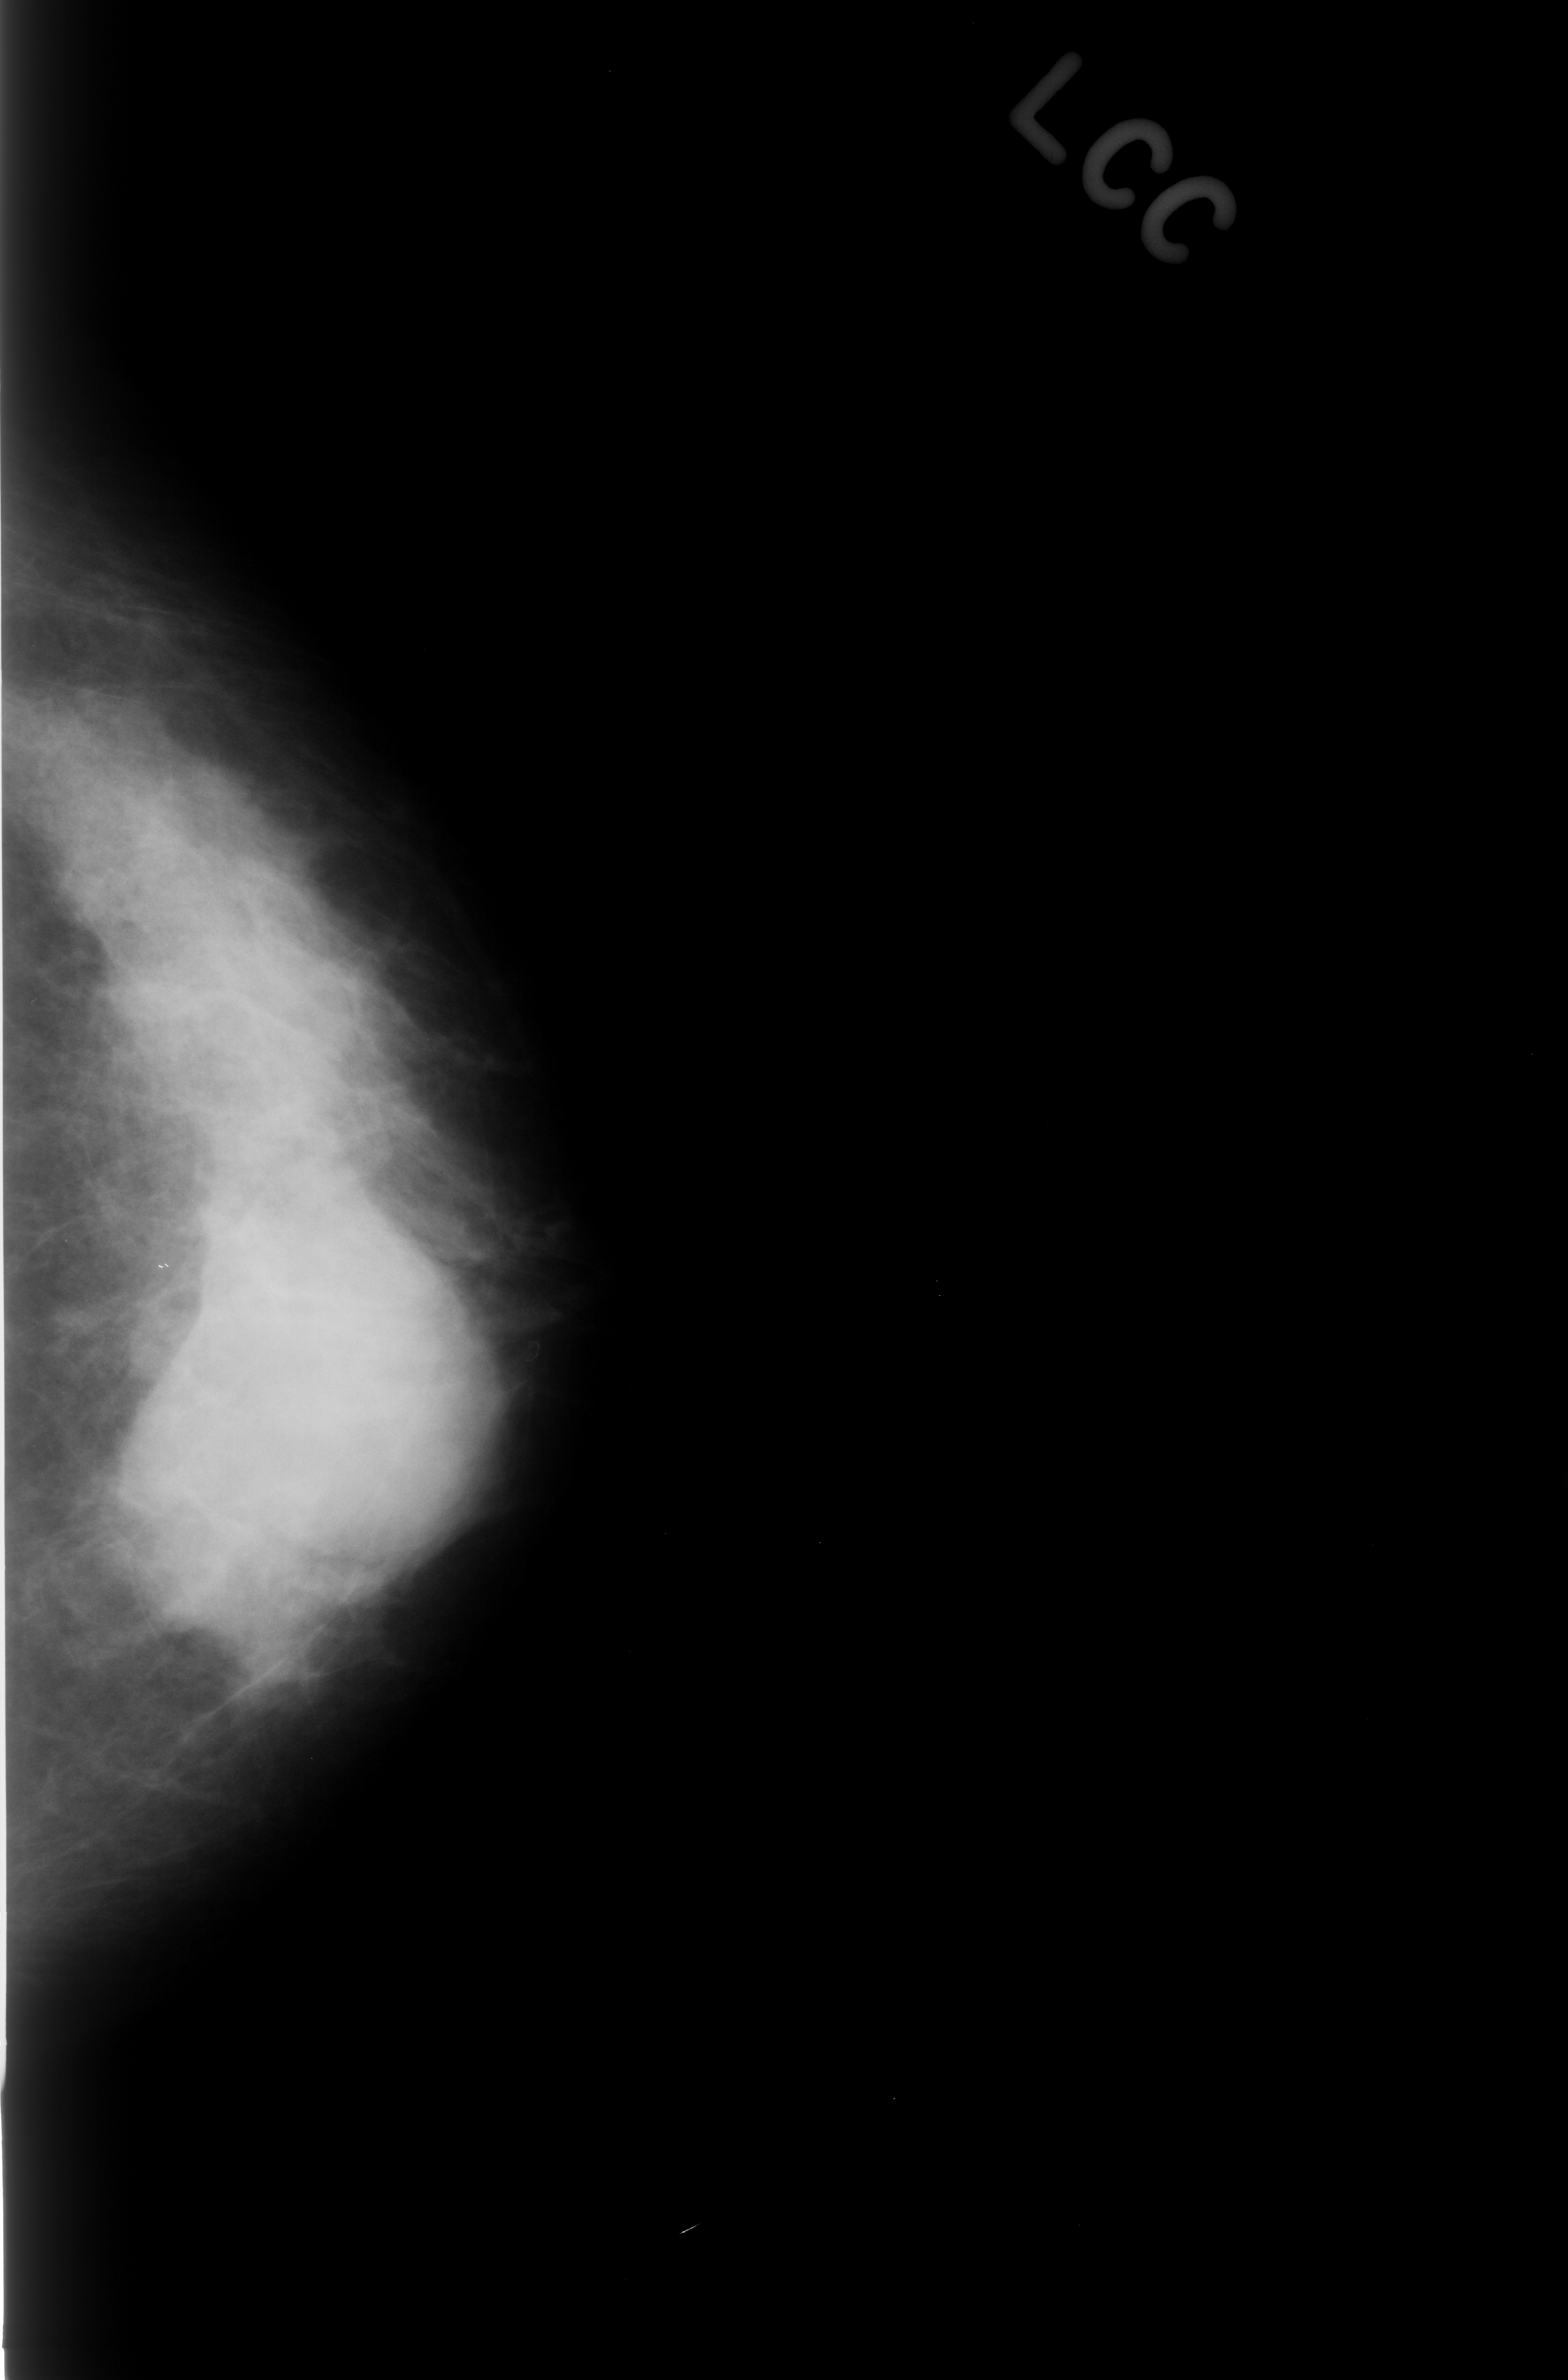
Scanned film-screen mammogram; left breast; CC view; breast composition: extremely dense (BI-RADS density category 4 of 4); 1568 × 2380 image matrix.
Expert-marked regions of interest on this film, with their recorded descriptors:
- mass, shape round, margins obscured; BI-RADS assessment category 4; subtlety rating 5 on a 1 (subtle) to 5 (obvious) scale; pathology result (as recorded, not read from the image): benign: bounding box [x1, y1, x2, y2] px = [231, 1224, 526, 1601]